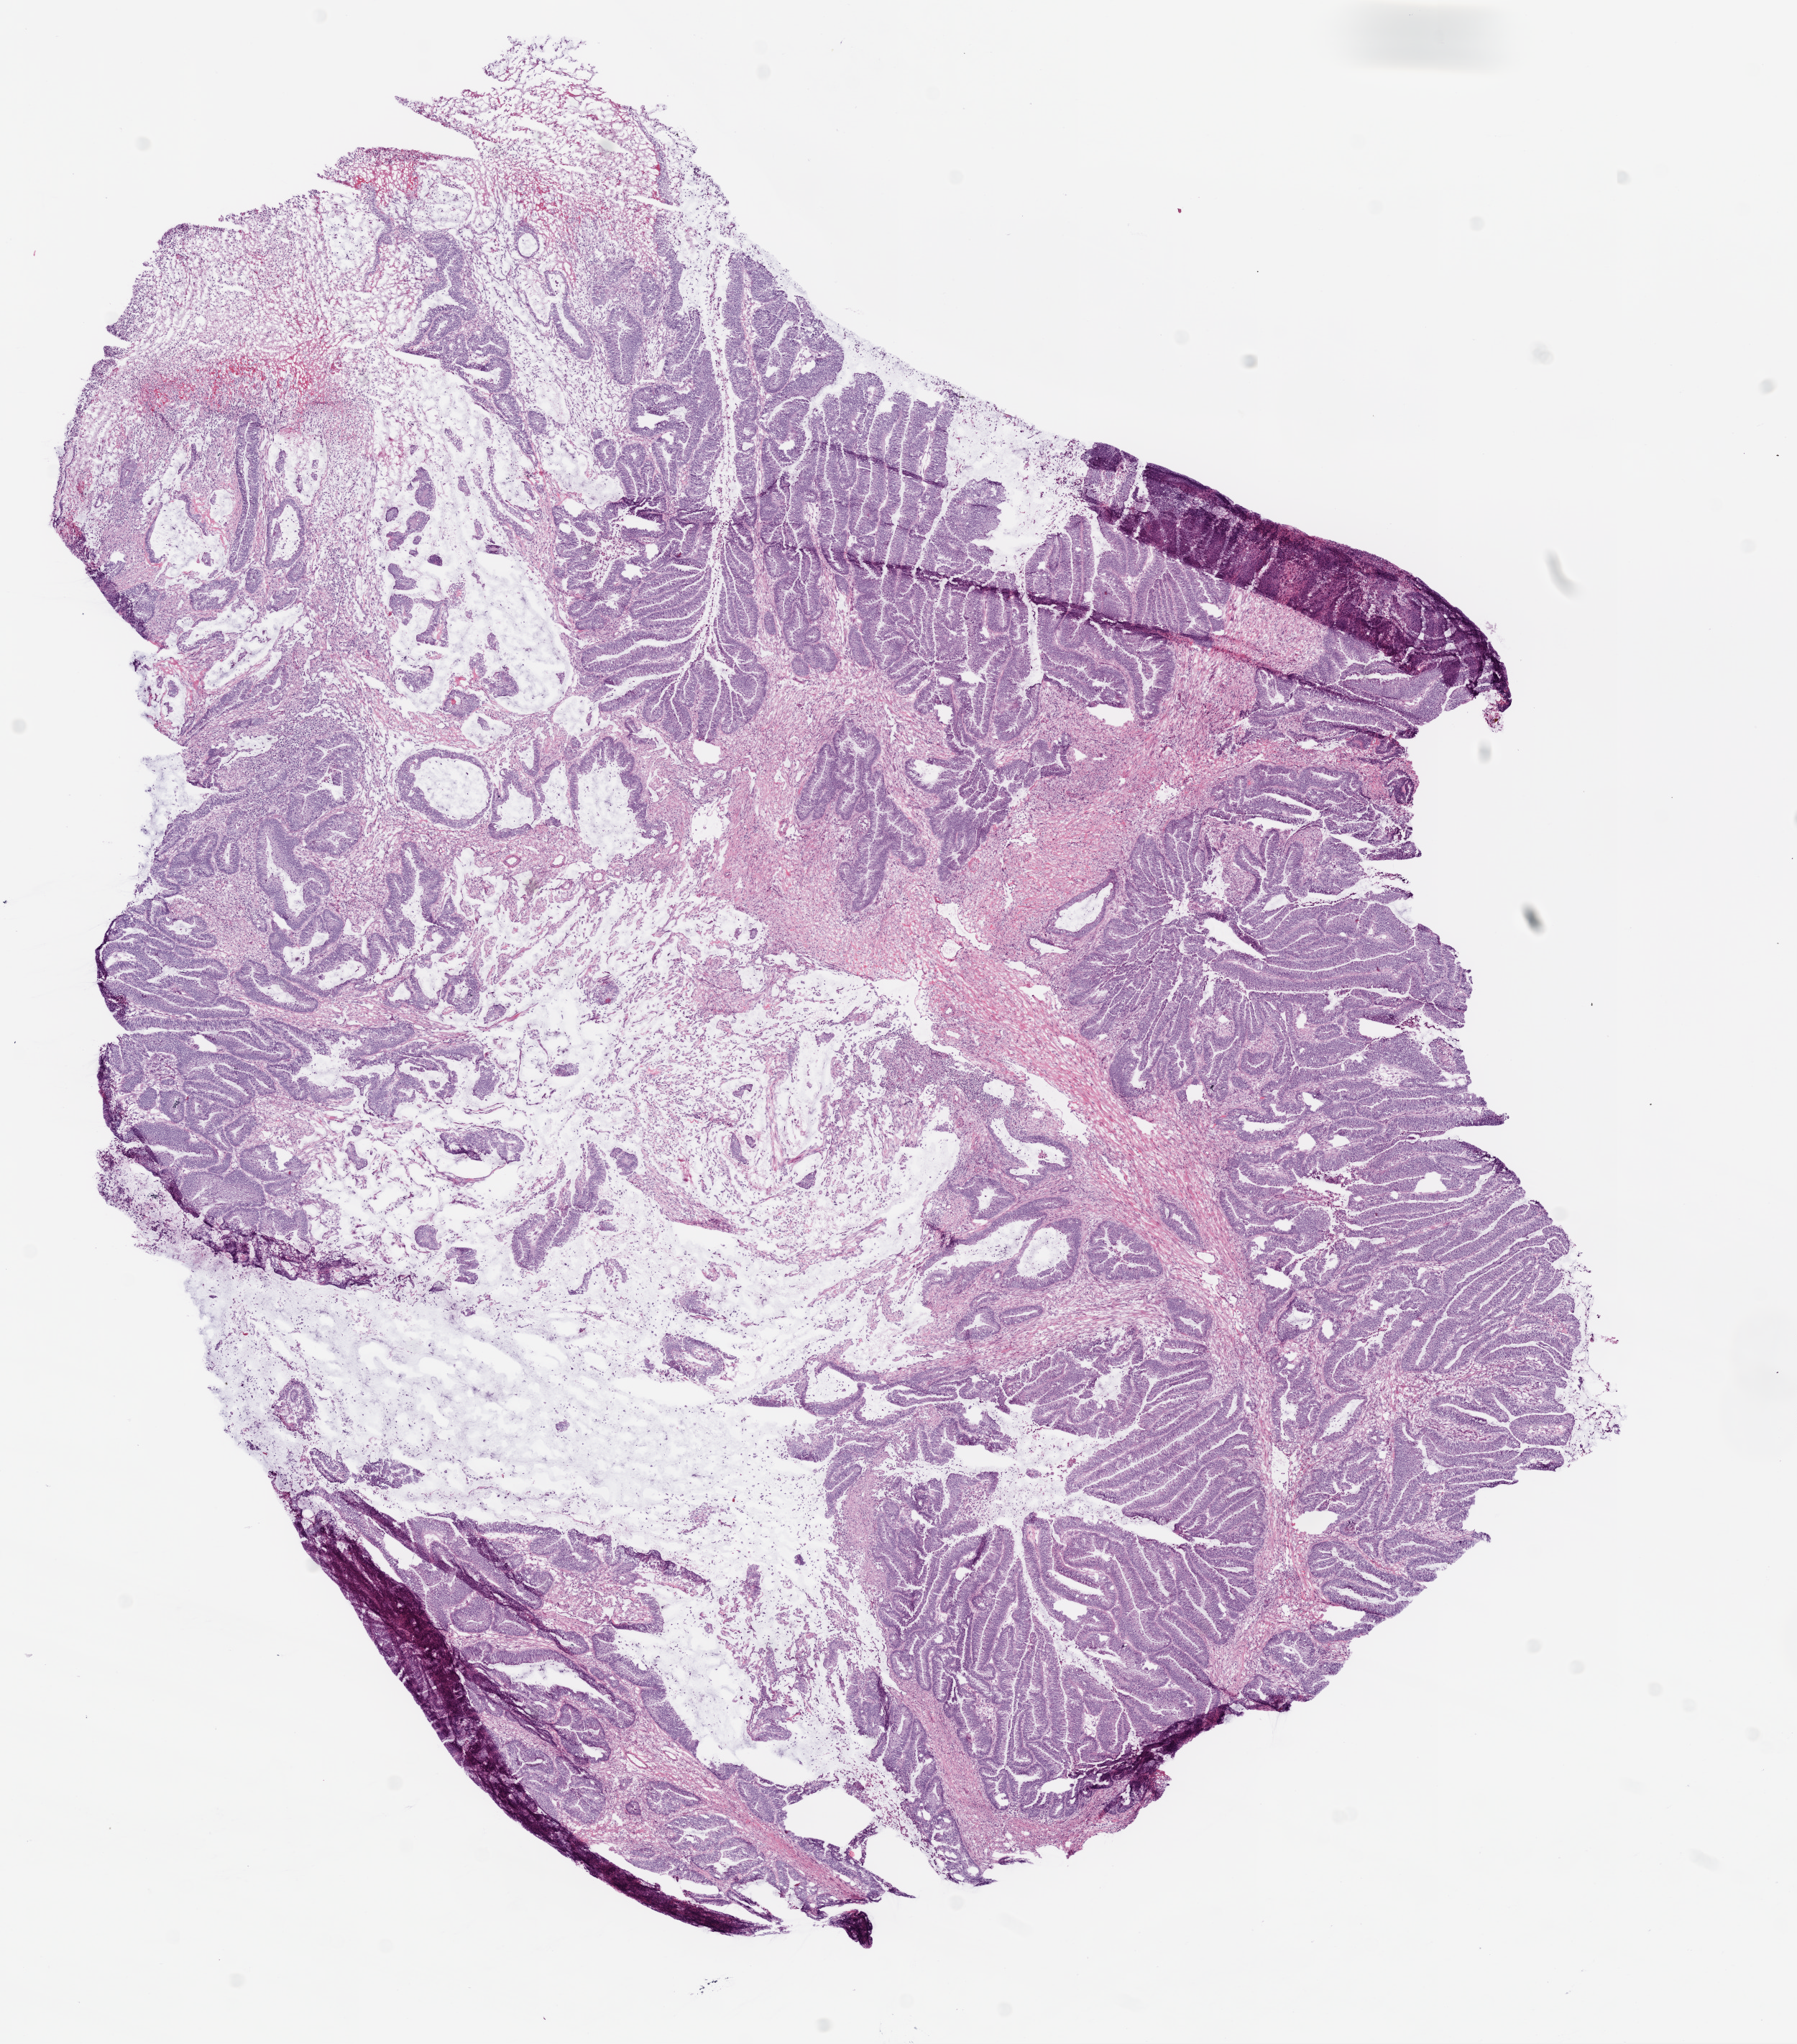
Hematoxylin and eosin (H&E) stained whole-slide image, low-resolution overview of the scanned area, about 10.0 x 11.4 mm (slide scanned at 20x), frozen section from the bottom of the tissue portion, primary tumour sample from the colon. Patient: female, age at initial diagnosis 81 years. Slide review estimates, as recorded: tumour cells 40%, tumour nuclei 60%, normal cells 0%, stromal cells 60%, necrosis 0%.
AJCC pathologic stage: IIA. TNM: T3 N0 M0. Diagnosis: Adenocarcinoma, NOS. Lymph nodes positive (case pathology): 0 of 26 examined.